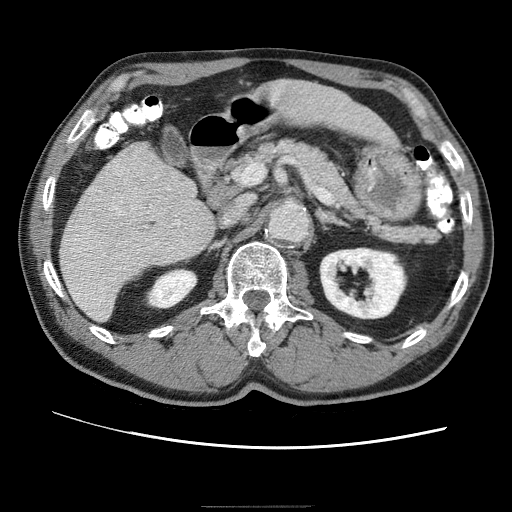
Contrast-enhanced abdominal CT (liver protocol), one axial slice; position 22 of 75 along the scan axis; reconstruction kernel STANDARD; one of 2 acquisitions stored at this slice position; soft-tissue window (W 400 / L 40 HU); 2.5 mm slice thickness; 512 × 512 image matrix. From the clinical record (not read from this slice): diagnosis: hepatocellular carcinoma (patient treated with transarterial chemoembolisation; whether this scan precedes or follows treatment is not stated here); TNM stage (as recorded): Stage-II; Child-Pugh class: A; tumour differentiation: well differentiated; tumour size: 2 cm.
Structures marked on this image (semi-automatically segmented with operator editing):
- liver parenchyma outside the tumour (the mass and vessels are separate outlines, so this box may not span the whole liver): bounding box (x1, y1, x2, y2) in pixels: (60, 80, 348, 320)
- liver vessels: (76, 161, 121, 257)